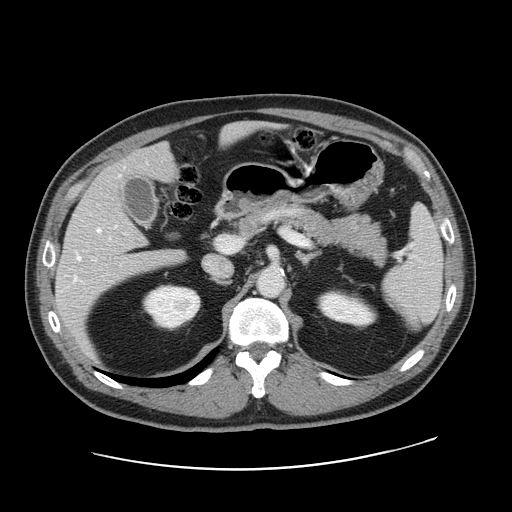
Contrast-enhanced abdominal CT, one axial slice; slice 94 of 178 in the series (ordered by position); 120 kVp; intravenous contrast given; soft-tissue window (W 400 / L 40 HU); 2.5 mm slice thickness; 512 × 512 image matrix. Male patient, age 63 years. Case-level facts recorded for this patient, not image findings: diagnosis: colorectal cancer liver metastases, imaged before liver resection; multiple liver metastases: yes; largest metastasis: 8 cm; disease in both lobes: yes.
Structures marked on this image (expert manual segmentation):
- hepatic veins: bounding box (x1, y1, x2, y2) in pixels: (74, 175, 121, 280)
- liver: (56, 123, 263, 348)
- planned liver remnant (the part of the liver to remain after resection): (117, 124, 258, 183)
- portal vein (with intrahepatic branches): (93, 236, 242, 260)